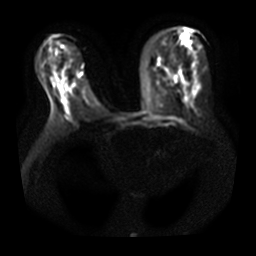
Breast MRI, one axial slice; slice 16 of 38 in the series (ordered by position); diffusion-weighted series; image 2 of 4 stored at this slice position (different b-values; order by instance number); 3 T; 256 × 256 image matrix. Female patient.
Structures marked on this image (expert manual segmentation):
- tumour on diffusion-weighted imaging: bounding box (x1, y1, x2, y2) in pixels: (77, 74, 81, 78)